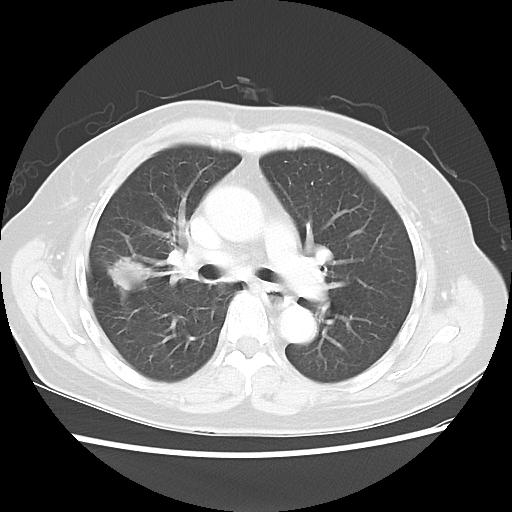
Chest CT, one axial slice; reconstruction kernel LUNG; lung window (W 1500 / L -600 HU); 512 × 512 image matrix, field of view 342 × 342 mm. Patient: female, 67 years. Case-level facts recorded for this patient, not image findings: clinical TNM (as recorded): T1c N1 M0.
Annotated regions visible in this slice (bounding box drawn by a radiologist):
- lung tumour (recorded histology: adenocarcinoma): bounding box (x1, y1, x2, y2) in pixels: (105, 244, 152, 300)